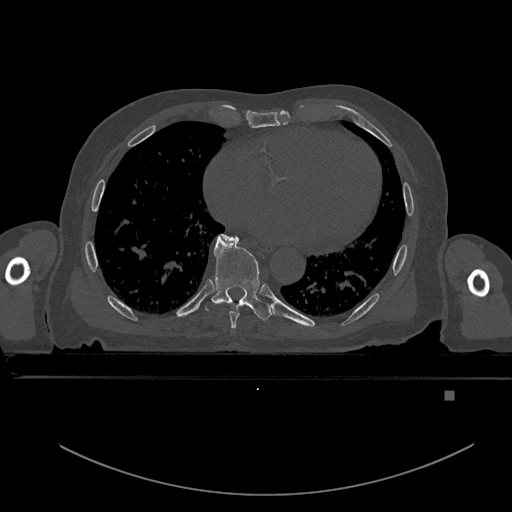
CT including the spine, one axial slice; bone window (W 1800 / L 400 HU); 0.5 mm slice thickness; 512 × 512 image matrix. Patient: male, 82 years. From the clinical record (not read from this slice): primary cancer: prostate; vertebrae with lytic lesions (as recorded): T11, T9, T8, T2.
Outlined on this slice (semi-automatic segmentation, software-assisted and operator-edited):
- T7 vertebra: bounding box [x1, y1, x2, y2] px = [224, 235, 239, 328]
- T8 vertebra: [212, 235, 273, 321]